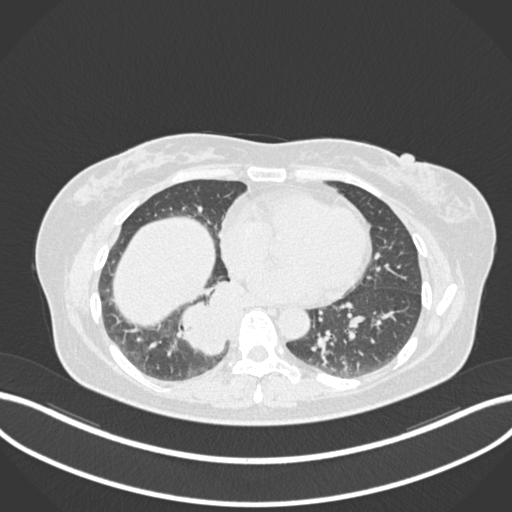
Chest CT, one axial slice; position 558 of 677 along the scan axis; 120 kVp; lung window (W 1500 / L -600 HU); 512 × 512 image matrix, field of view 400 × 400 mm. Patient: female, 54 years. From the clinical record (not read from this slice): clinical TNM (as recorded): T4 N0 M0.
Outlined on this slice (rectangle marked by the reading radiologist):
- lung tumour (recorded histology: adenocarcinoma): bounding box [x1, y1, x2, y2] px = [173, 274, 249, 357]